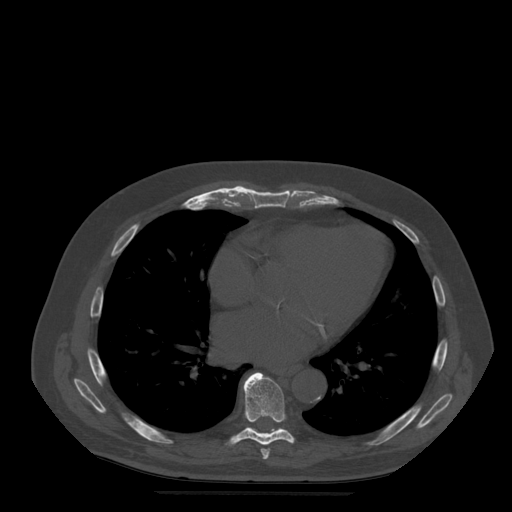
CT including the spine, one axial slice. Position 311 of 522 along the scan axis. Bone window (W 1800 / L 400 HU). 512 × 512 image matrix, field of view 420 × 420 mm. Patient age 72 years. From the clinical record (not read from this slice): primary cancer: prostate.
Structures marked on this image (semi-automatic segmentation, software-assisted and operator-edited):
- T7 vertebra: bounding box <261,449,270,460> (left, top, right, bottom; pixels)
- T8 vertebra: <230,373,295,446>
- T9 vertebra: <251,428,280,431>